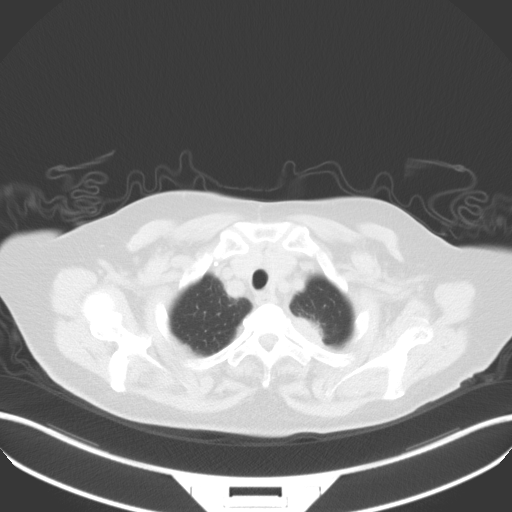
Chest CT, one axial slice; slice 37 of 42 in the series (ordered by position); lung window (W 1500 / L -600 HU); 6 mm slice thickness; 512 × 512 image matrix, field of view 400 × 400 mm. Patient: female, 81 years. From the clinical record (not read from this slice): clinical TNM (as recorded): T2a N0 M0.
Annotated regions visible in this slice (rectangle marked by the reading radiologist):
- lung tumour (recorded histology: adenocarcinoma): bounding box (x1, y1, x2, y2) in pixels: (293, 309, 323, 348)